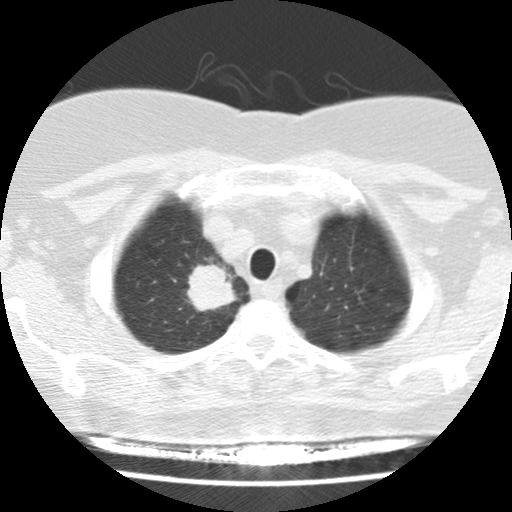
Chest CT (low-dose screening protocol), one axial image, baseline annual screen, lung window (W 1500 / L -600 HU), 2.5 mm slice thickness, standard (soft-tissue) reconstruction kernel (STANDARD), 120 kVp. Female, age 58 years at enrolment. Former smoker at enrolment.
Lesion marked by an expert reader, bounding box [x1, y1, x2, y2] px = [169, 249, 247, 326]. The exam's reader record, not a measurement of the box and not confirmed to be the same lesion: non-calcified nodule or mass ≥4 mm, right upper lobe, 28 × 24 mm, spiculated (stellate) margins, soft tissue attenuation. Official screen result: positive, change unspecified: nodule(s) >= 4 mm or enlarging nodule(s), mass(es), or other non-specific abnormalities suspicious for lung cancer. Participant outcome: lung cancer diagnosed 40 days after this screen — adenocarcinoma, NOS, right upper lobe, poorly differentiated (G3), stage IB (AJCC 6th edition), 29 mm at pathology.